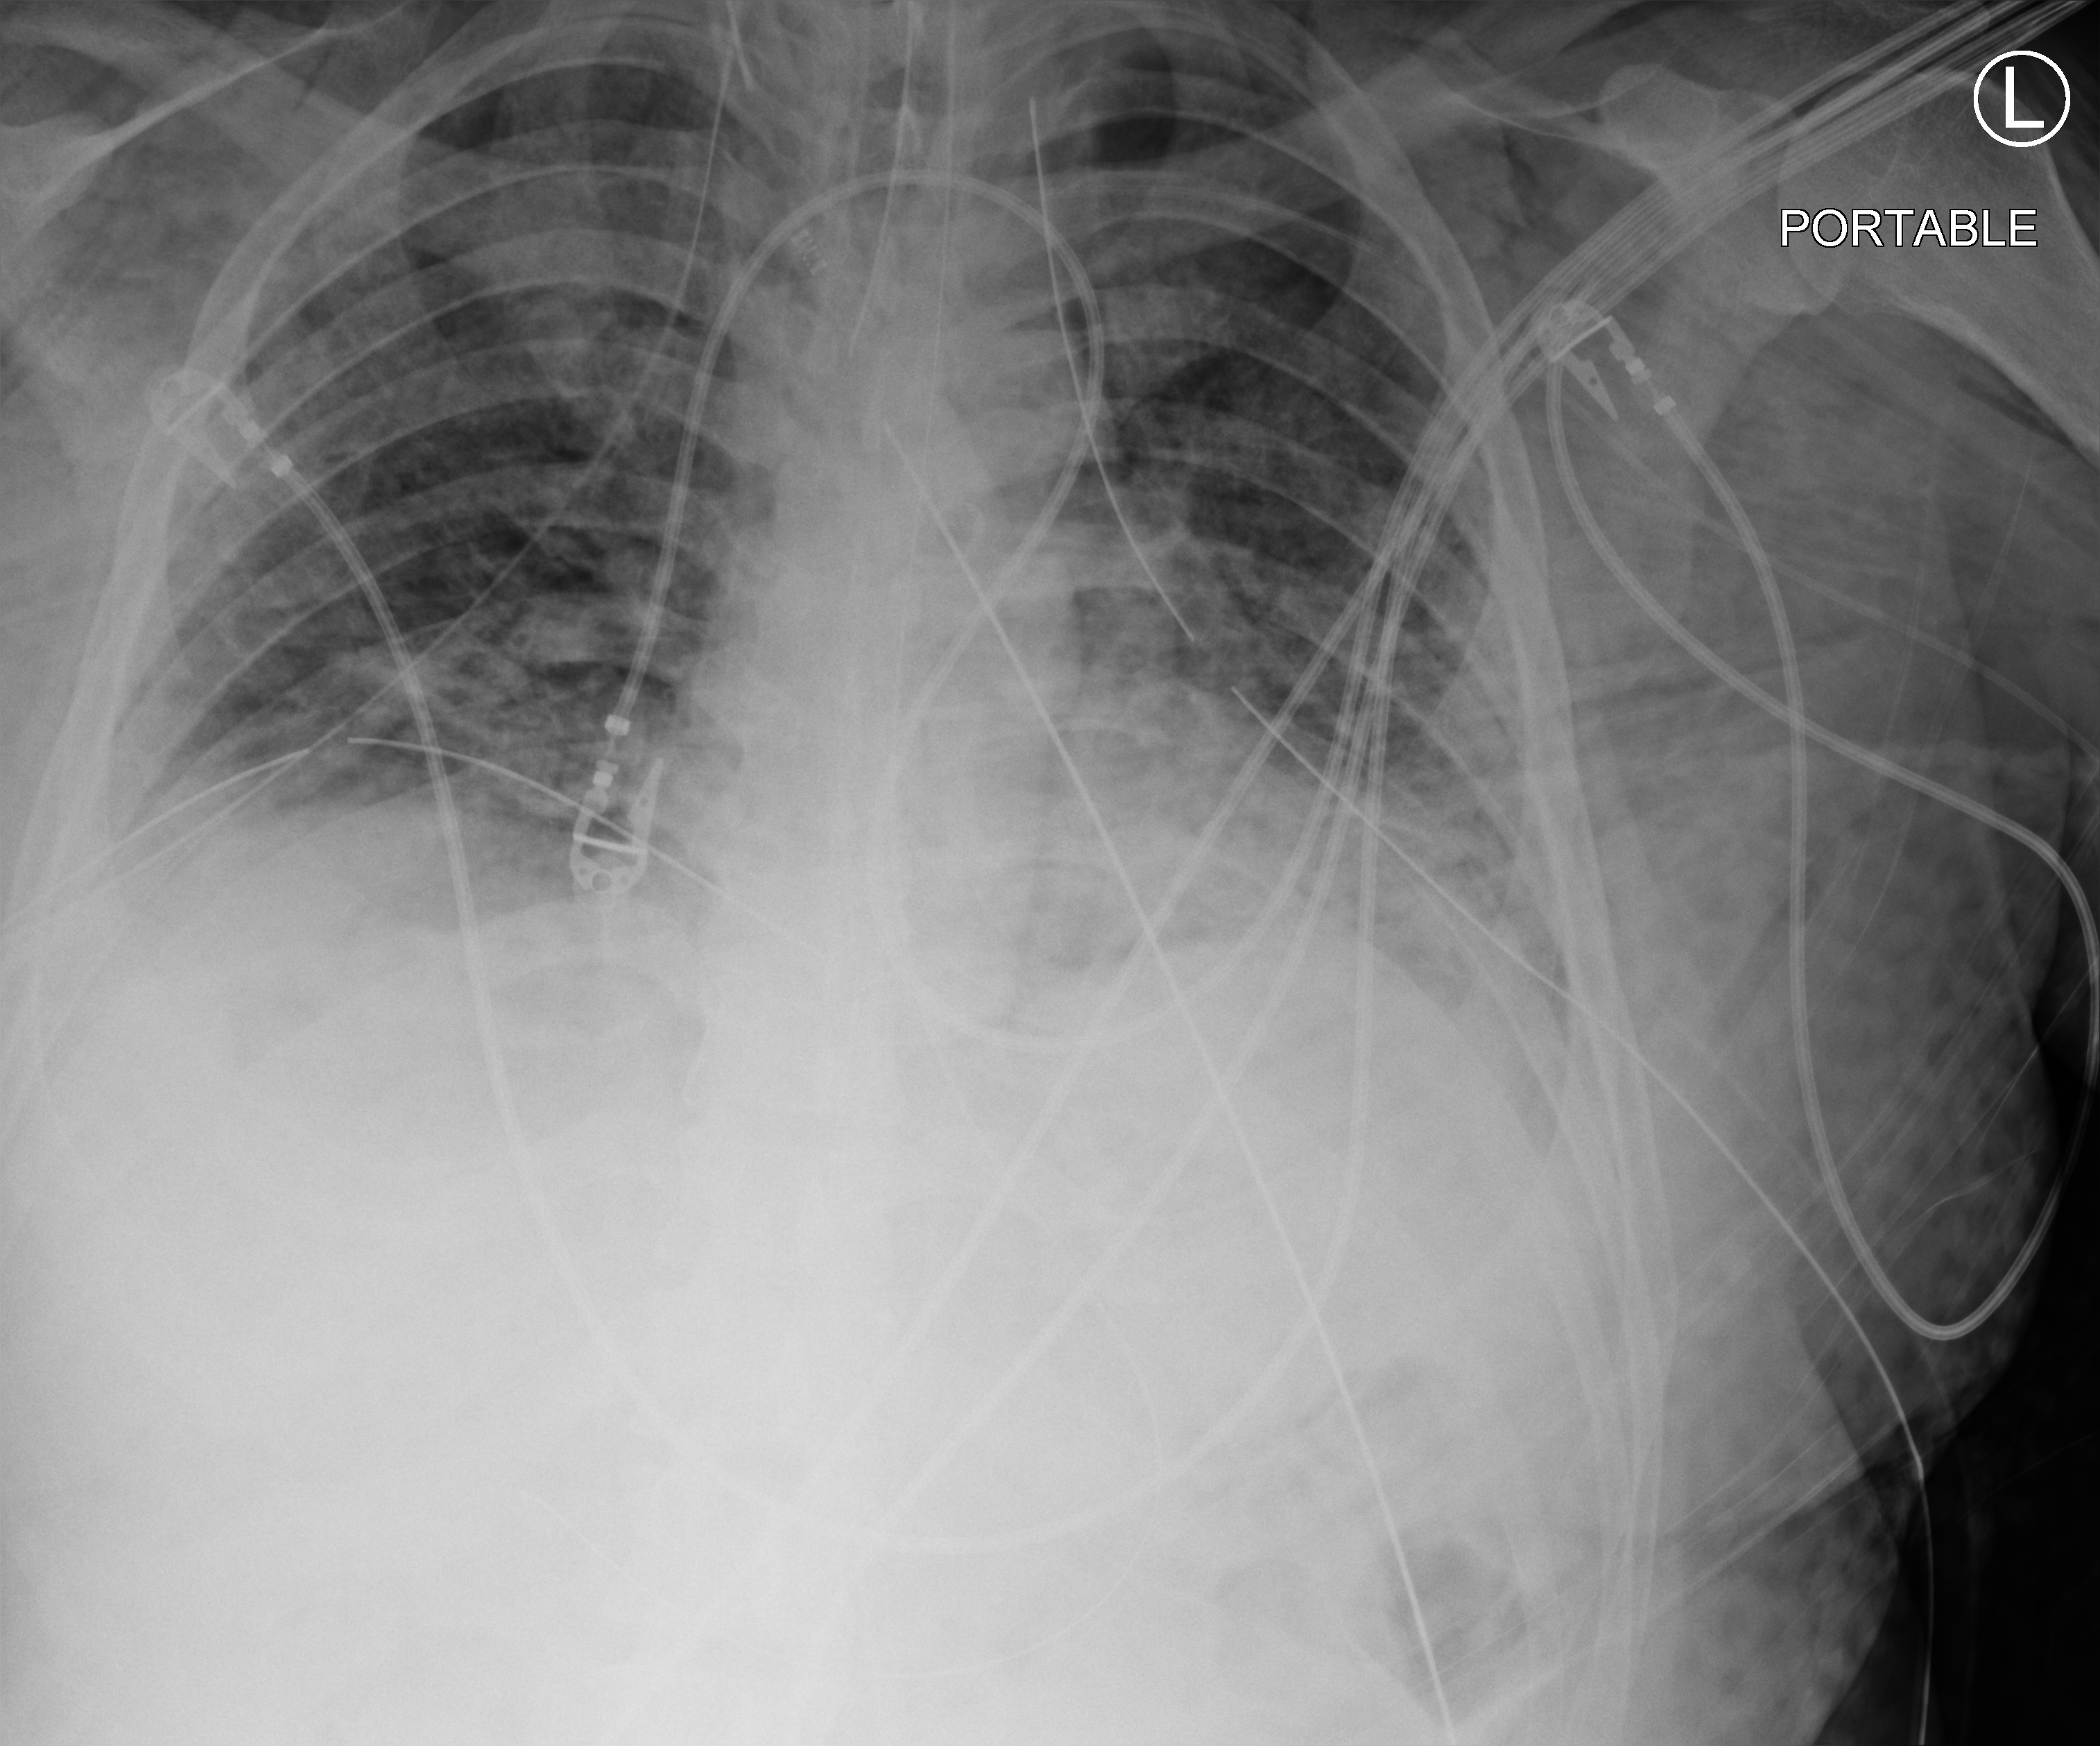
Portable chest radiograph. Male patient hospitalised with COVID-19, age 18–59 years.
Admission-level facts for this patient (not findings on this image; timing relative to this image not recorded):
- mechanically ventilated during this hospital stay: yes